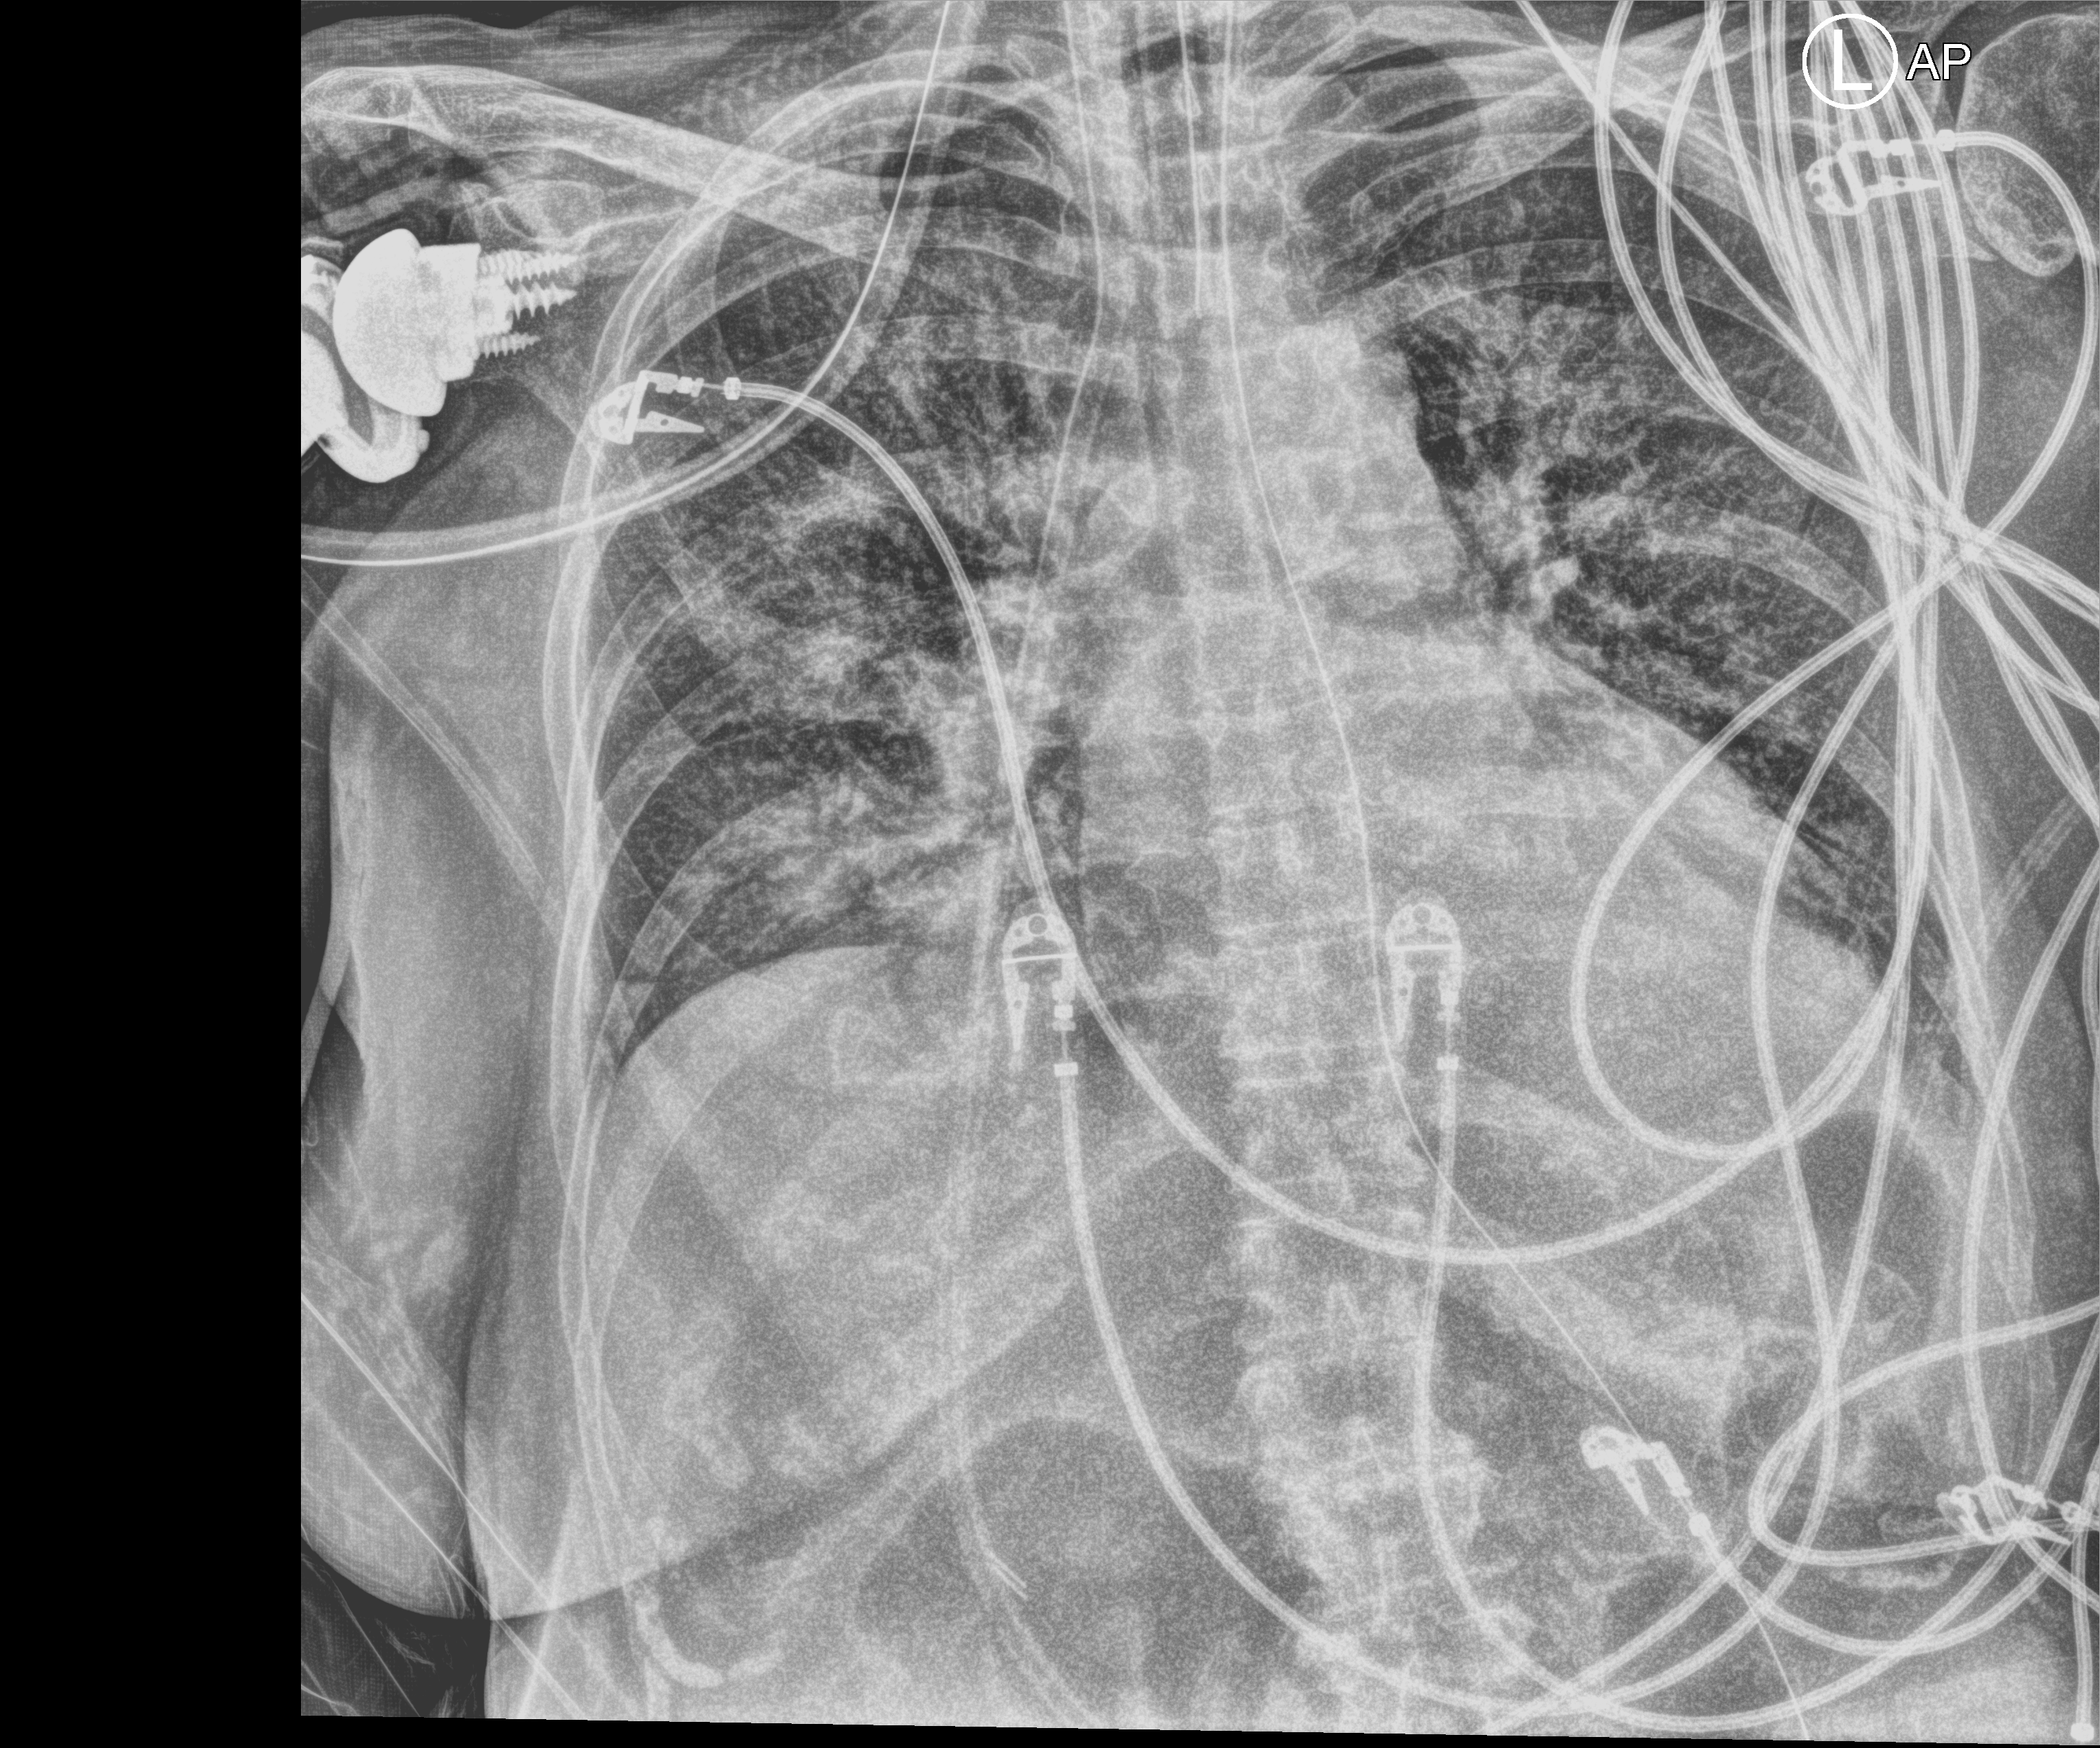
Bedside chest radiograph (computed radiography), anteroposterior (AP) projection. Female patient hospitalised with COVID-19, age 60–74 years.
Hospital-stay facts (about this admission, not read from this image; timing relative to this image not recorded): admitted to intensive care during this hospital stay: yes.